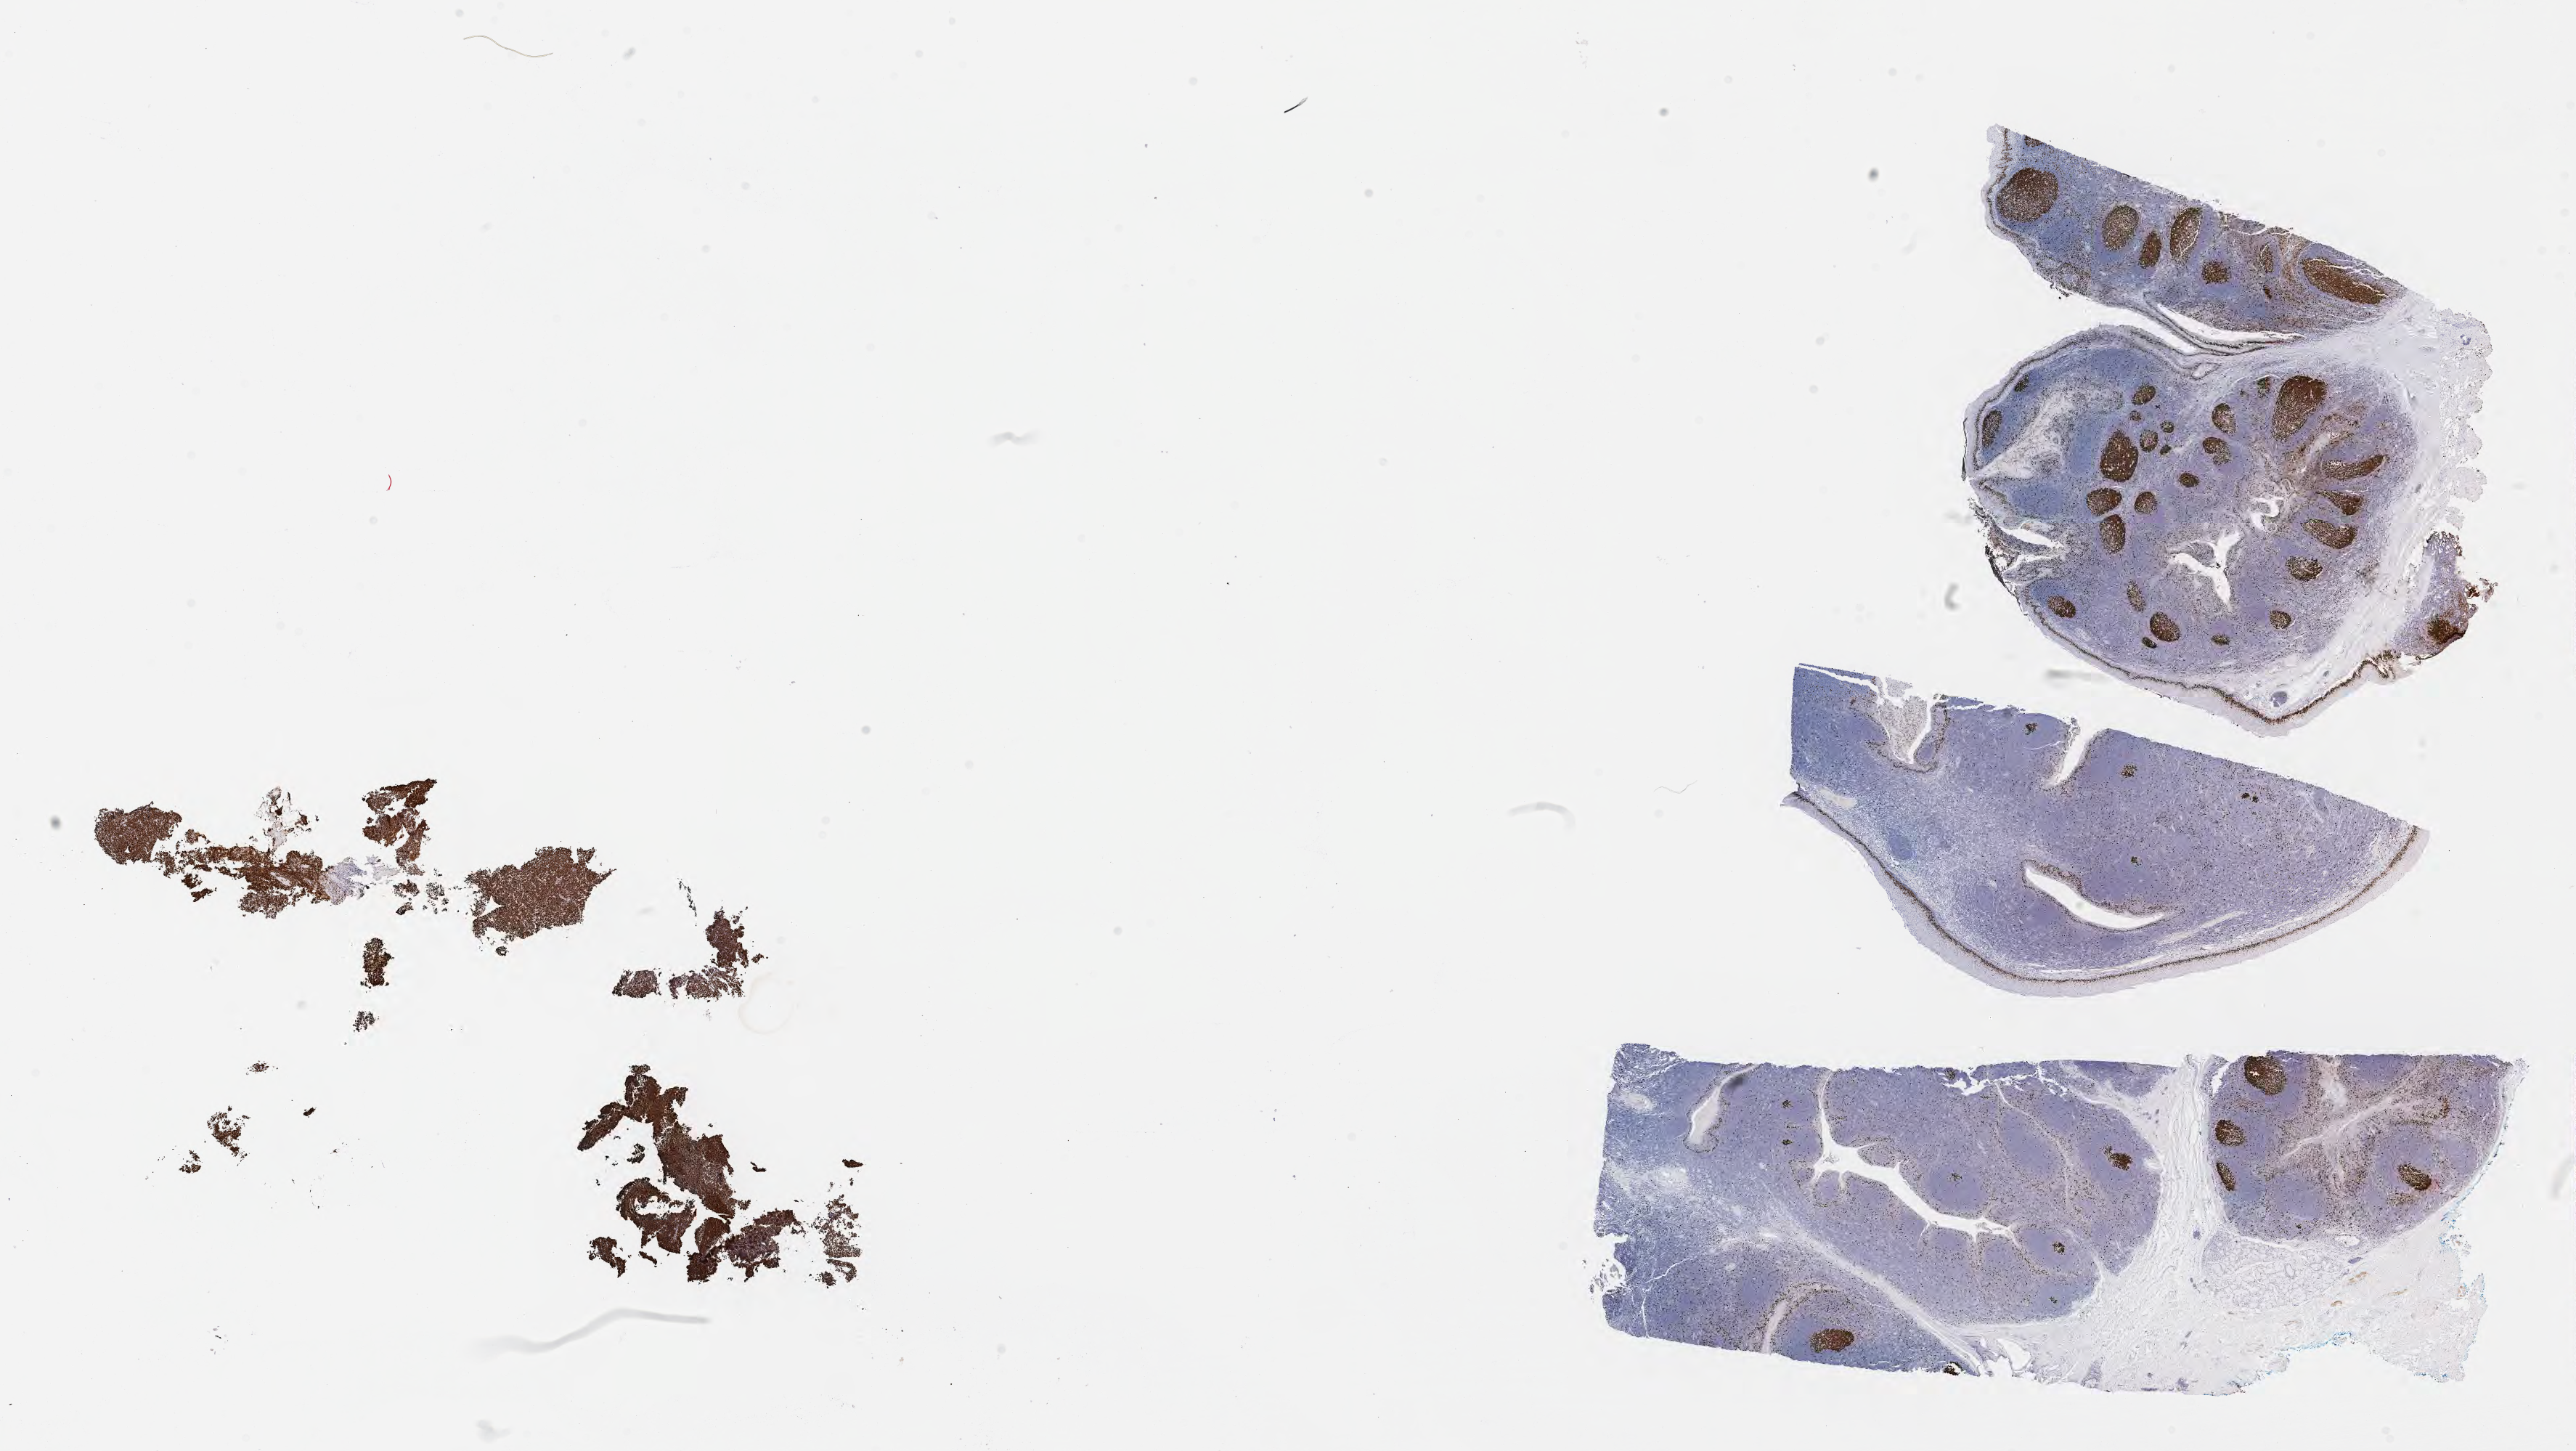
Whole-slide image, immunohistochemical stain for Ki-67 — a low-resolution overview of the entire scanned area, about 28.7 x 16.1 mm; tumor tissue; site: cranium. Female, age 1 years at initial diagnosis.
Histologic diagnosis: Burkitt lymphoma, NOS.